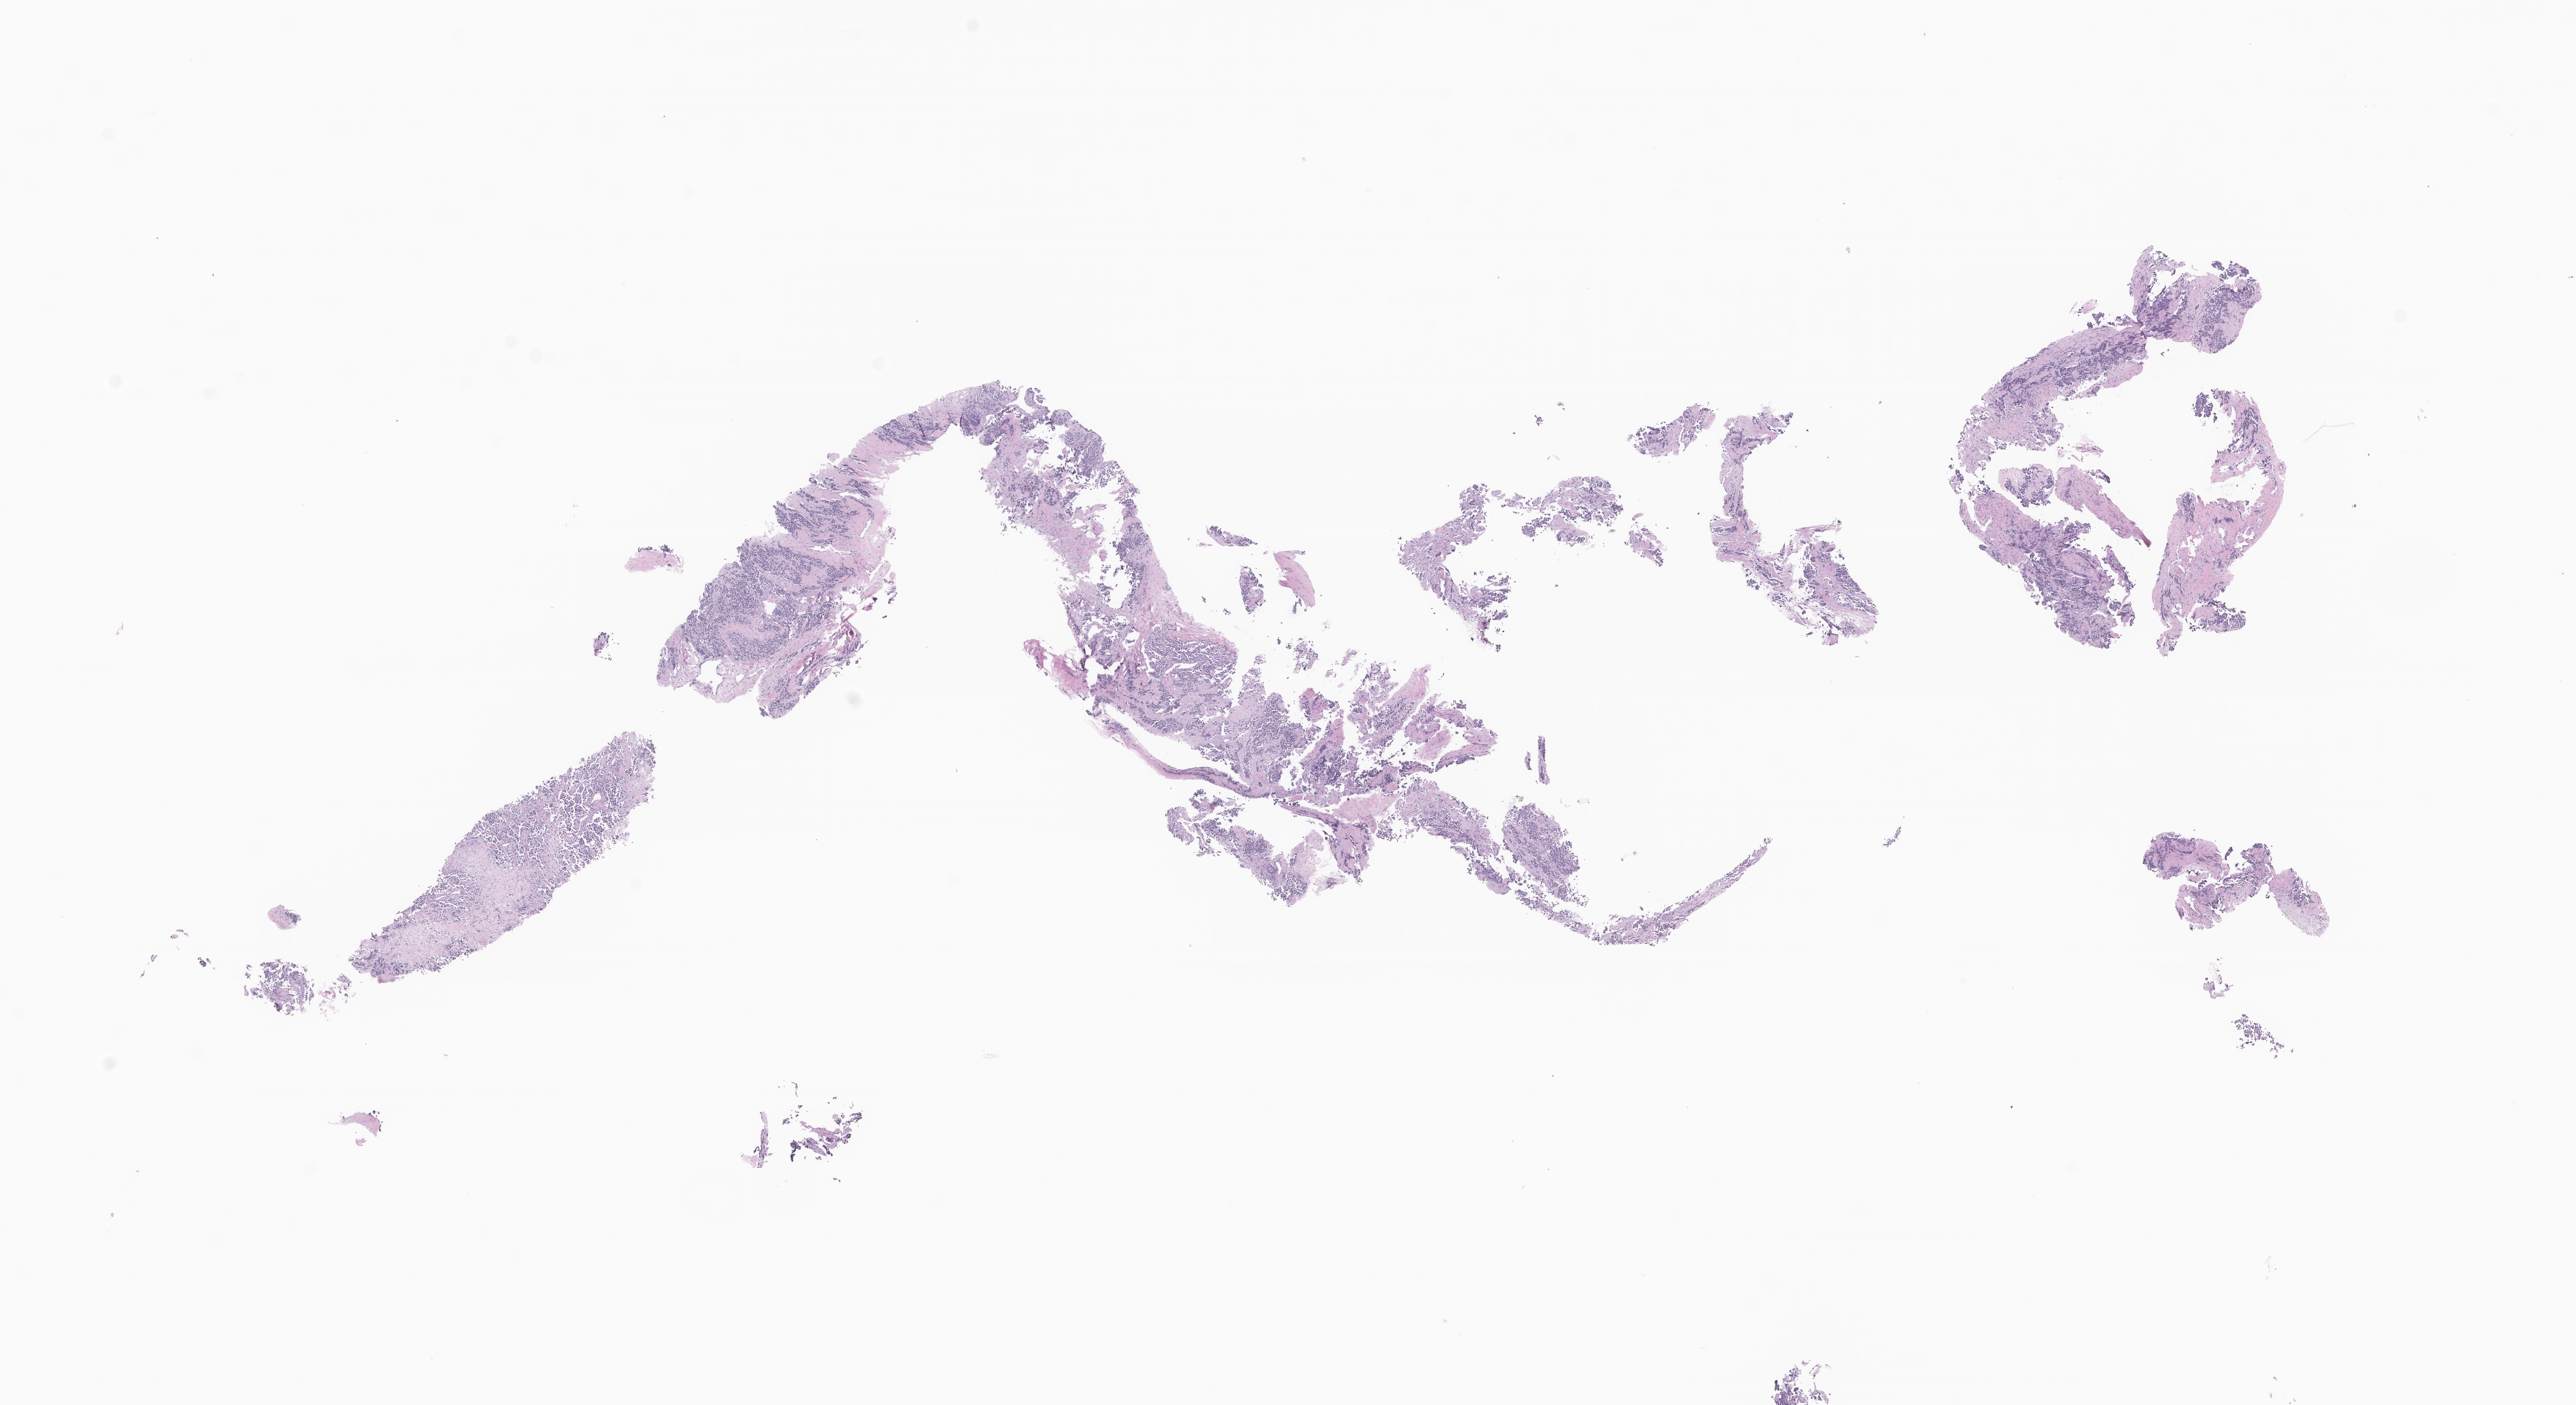
Whole-slide image, H&E stain of tumor tissue from the soft tissue, shown as a low-resolution overview of the whole scanned area (about 19.2 x 10.5 mm); FFPE section. Male patient, age 202 months (16 years 10 months).
Recorded diagnosis: Rhabdomyosarcoma, NOS.